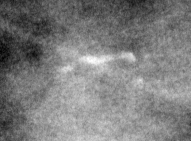
Cropped region of a digitized screen-film mammogram centred on a radiologist-marked abnormality, left breast, CC view.
- Finding: calcifications, morphology fine linear branching, distribution linear; BI-RADS assessment category 4; pathology (as recorded): malignant.